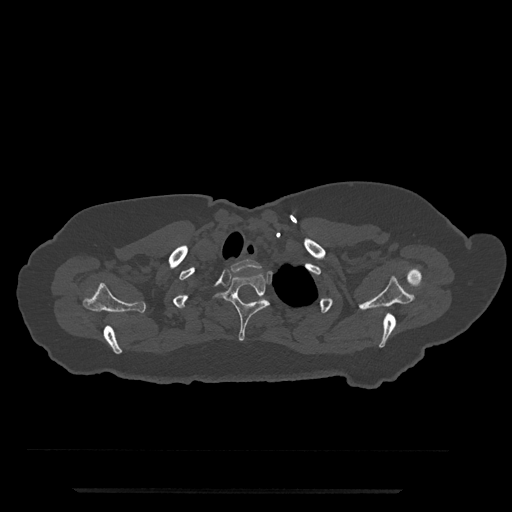
CT including the spine, one axial slice; slice 674 of 797 in the series (ordered by position); 120 kVp; bone window (W 1800 / L 400 HU); 0.5 mm slice thickness; 512 × 512 image matrix, field of view 440 × 440 mm. Patient: female, 51 years. From the clinical record (not read from this slice): primary cancer: neuro; vertebrae with lytic lesions (as recorded): T8.
Outlined on this slice (semi-automatic segmentation, software-assisted and operator-edited):
- T1 vertebra: bounding box [x1, y1, x2, y2] px = [231, 259, 261, 272]
- T2 vertebra: [215, 273, 270, 341]